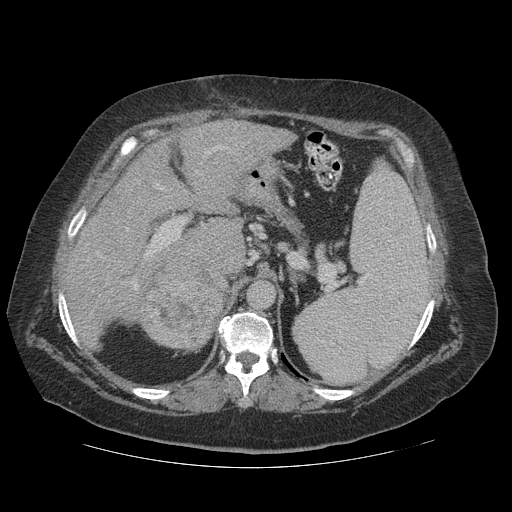
Contrast-enhanced abdominal CT (liver protocol), one axial slice. Slice 76 of 121 in the series (ordered by position). Soft-tissue window (W 400 / L 40 HU). 2.5 mm slice thickness. 512 × 512 image matrix, field of view 420 × 420 mm. From the clinical record (not read from this slice): diagnosis: hepatocellular carcinoma (patient treated with transarterial chemoembolisation; whether this scan precedes or follows treatment is not stated here); TNM stage (as recorded): Stage-IIIA; Child-Pugh class: A; tumour differentiation: well differentiated; tumour size: 7.4 cm.
Annotated regions visible in this slice (semi-automatic segmentation, software-assisted and operator-edited):
- liver parenchyma outside the tumour (the mass and vessels are separate outlines, so this box may not span the whole liver): bounding box (x1, y1, x2, y2) in pixels: (66, 120, 296, 332)
- mass: (133, 257, 226, 352)
- liver vessels: (96, 145, 237, 291)